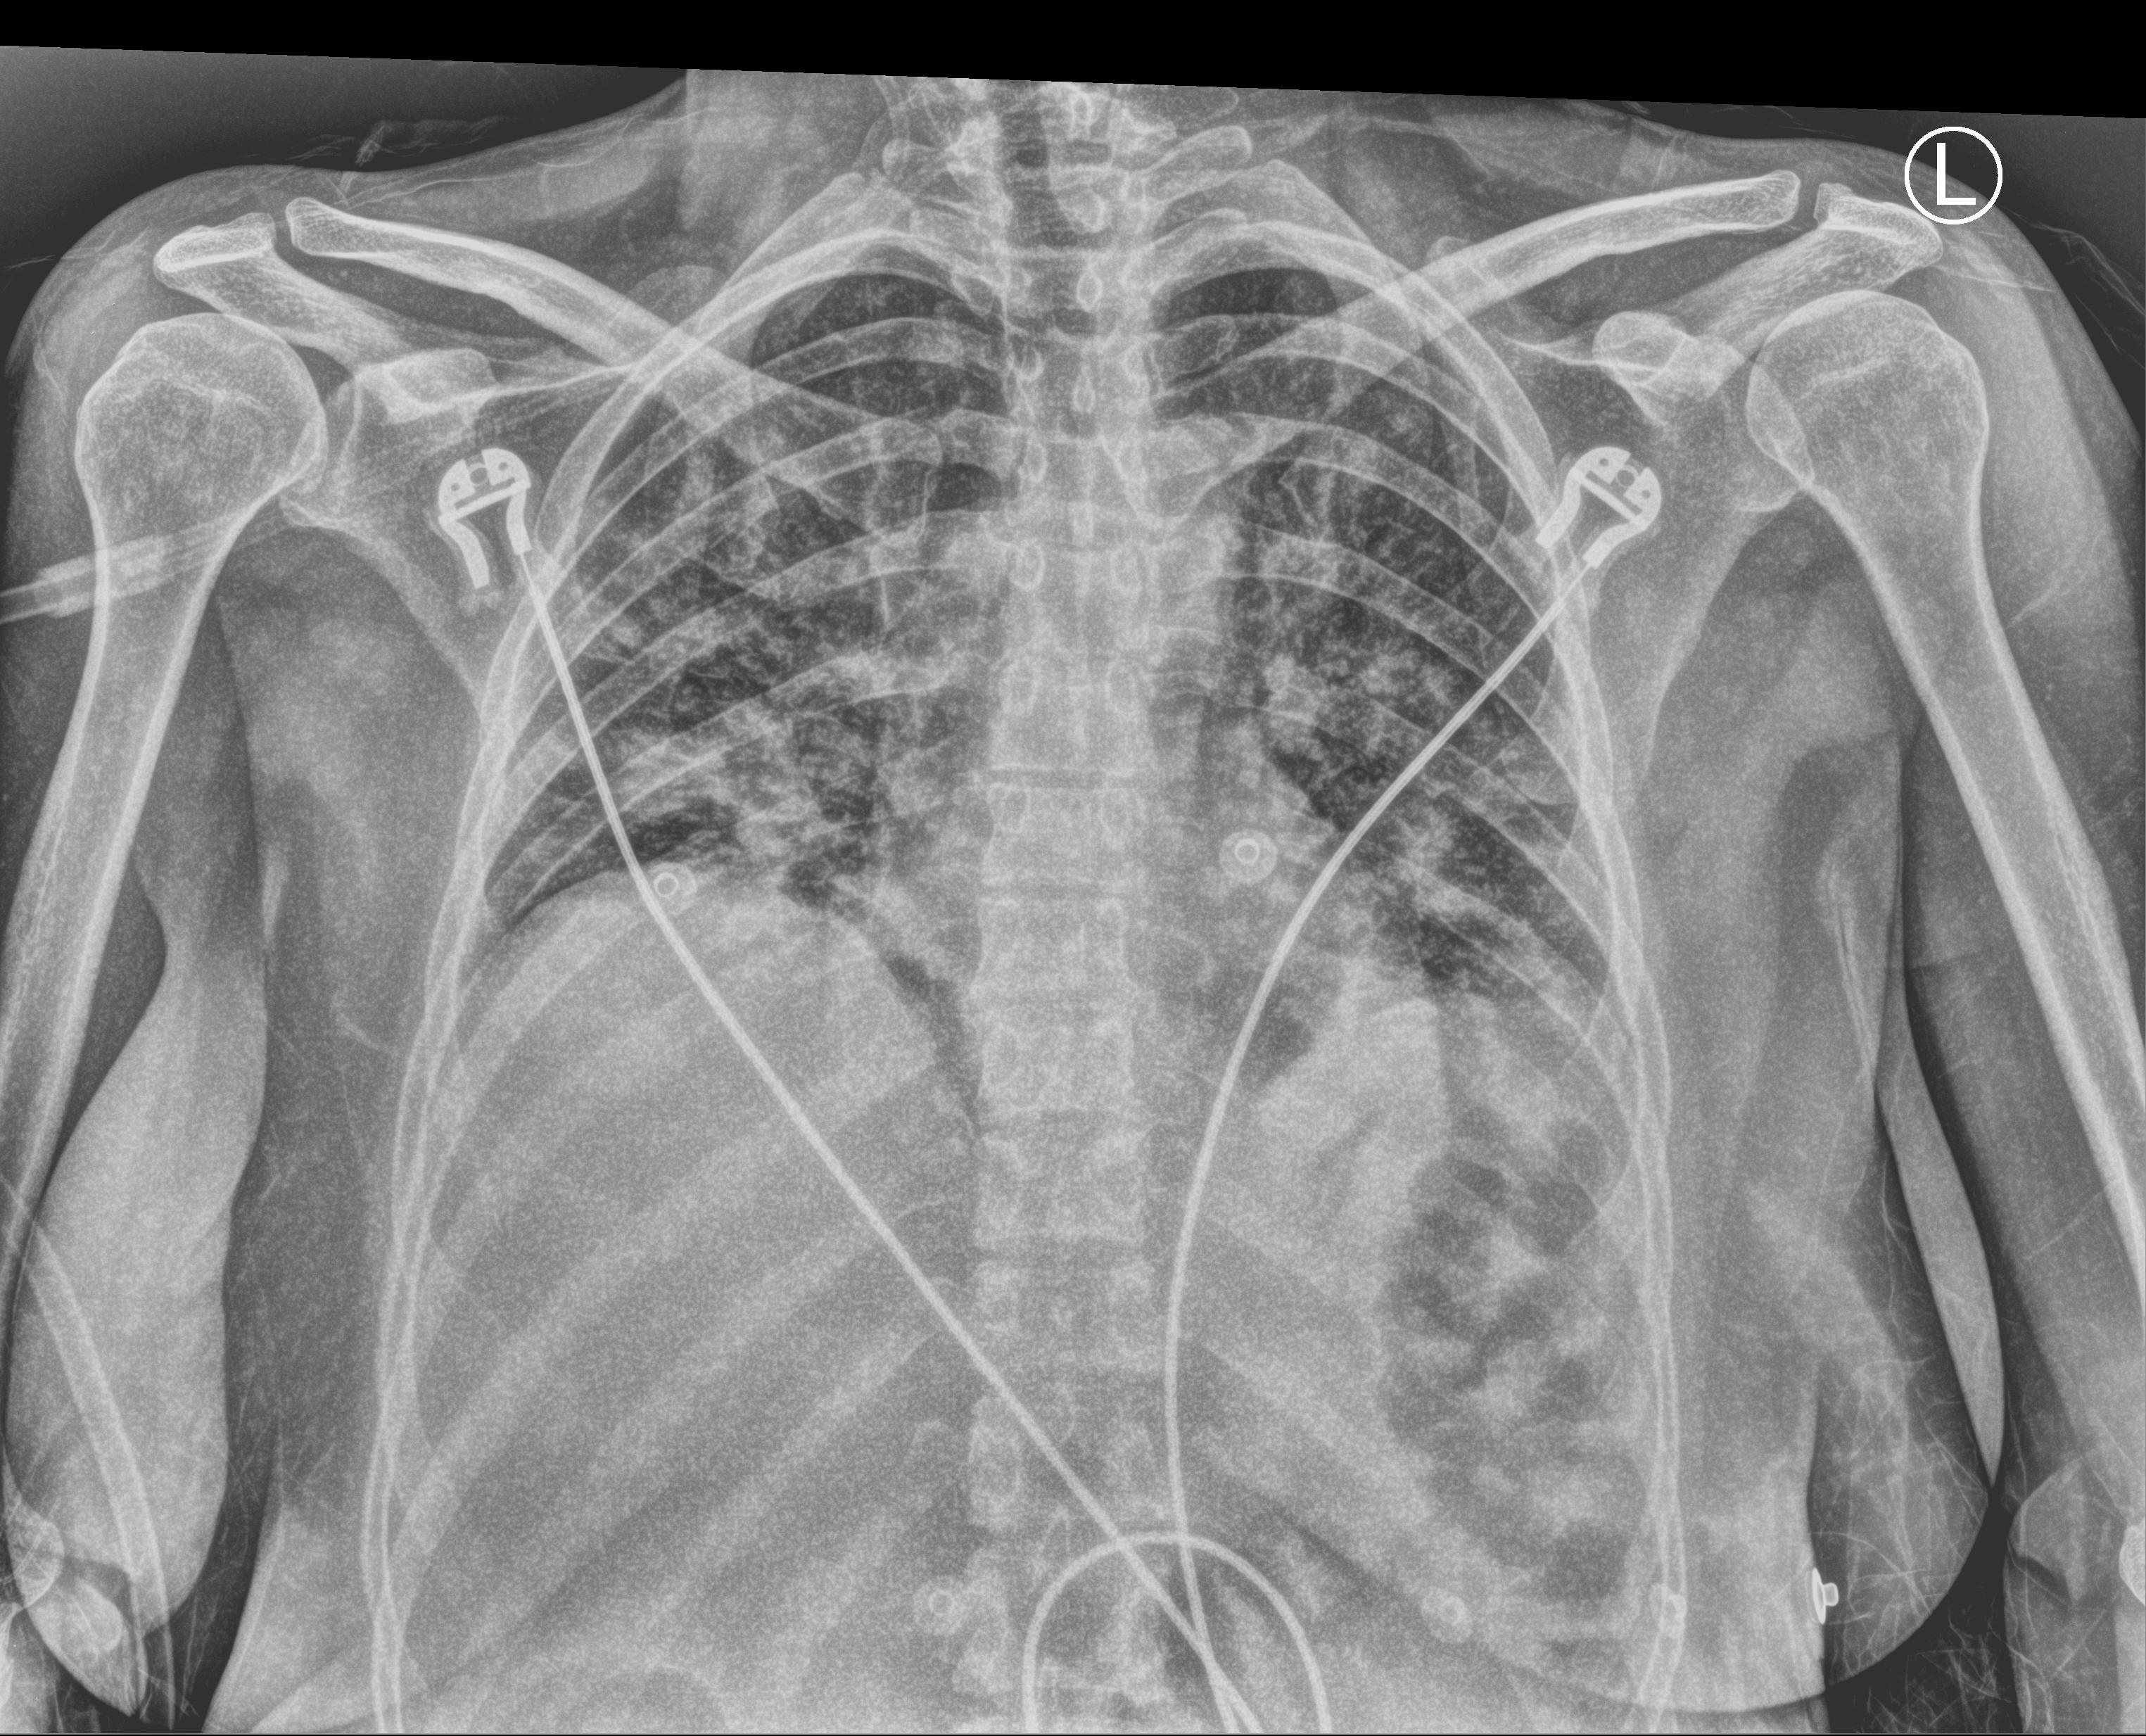
Bedside chest radiograph (computed radiography), anteroposterior (AP) projection. Patient hospitalised with COVID-19; female, aged 18–59 years.
Hospital-stay facts (about this admission, not read from this image; timing relative to this image not recorded): admitted to intensive care during this hospital stay: no.